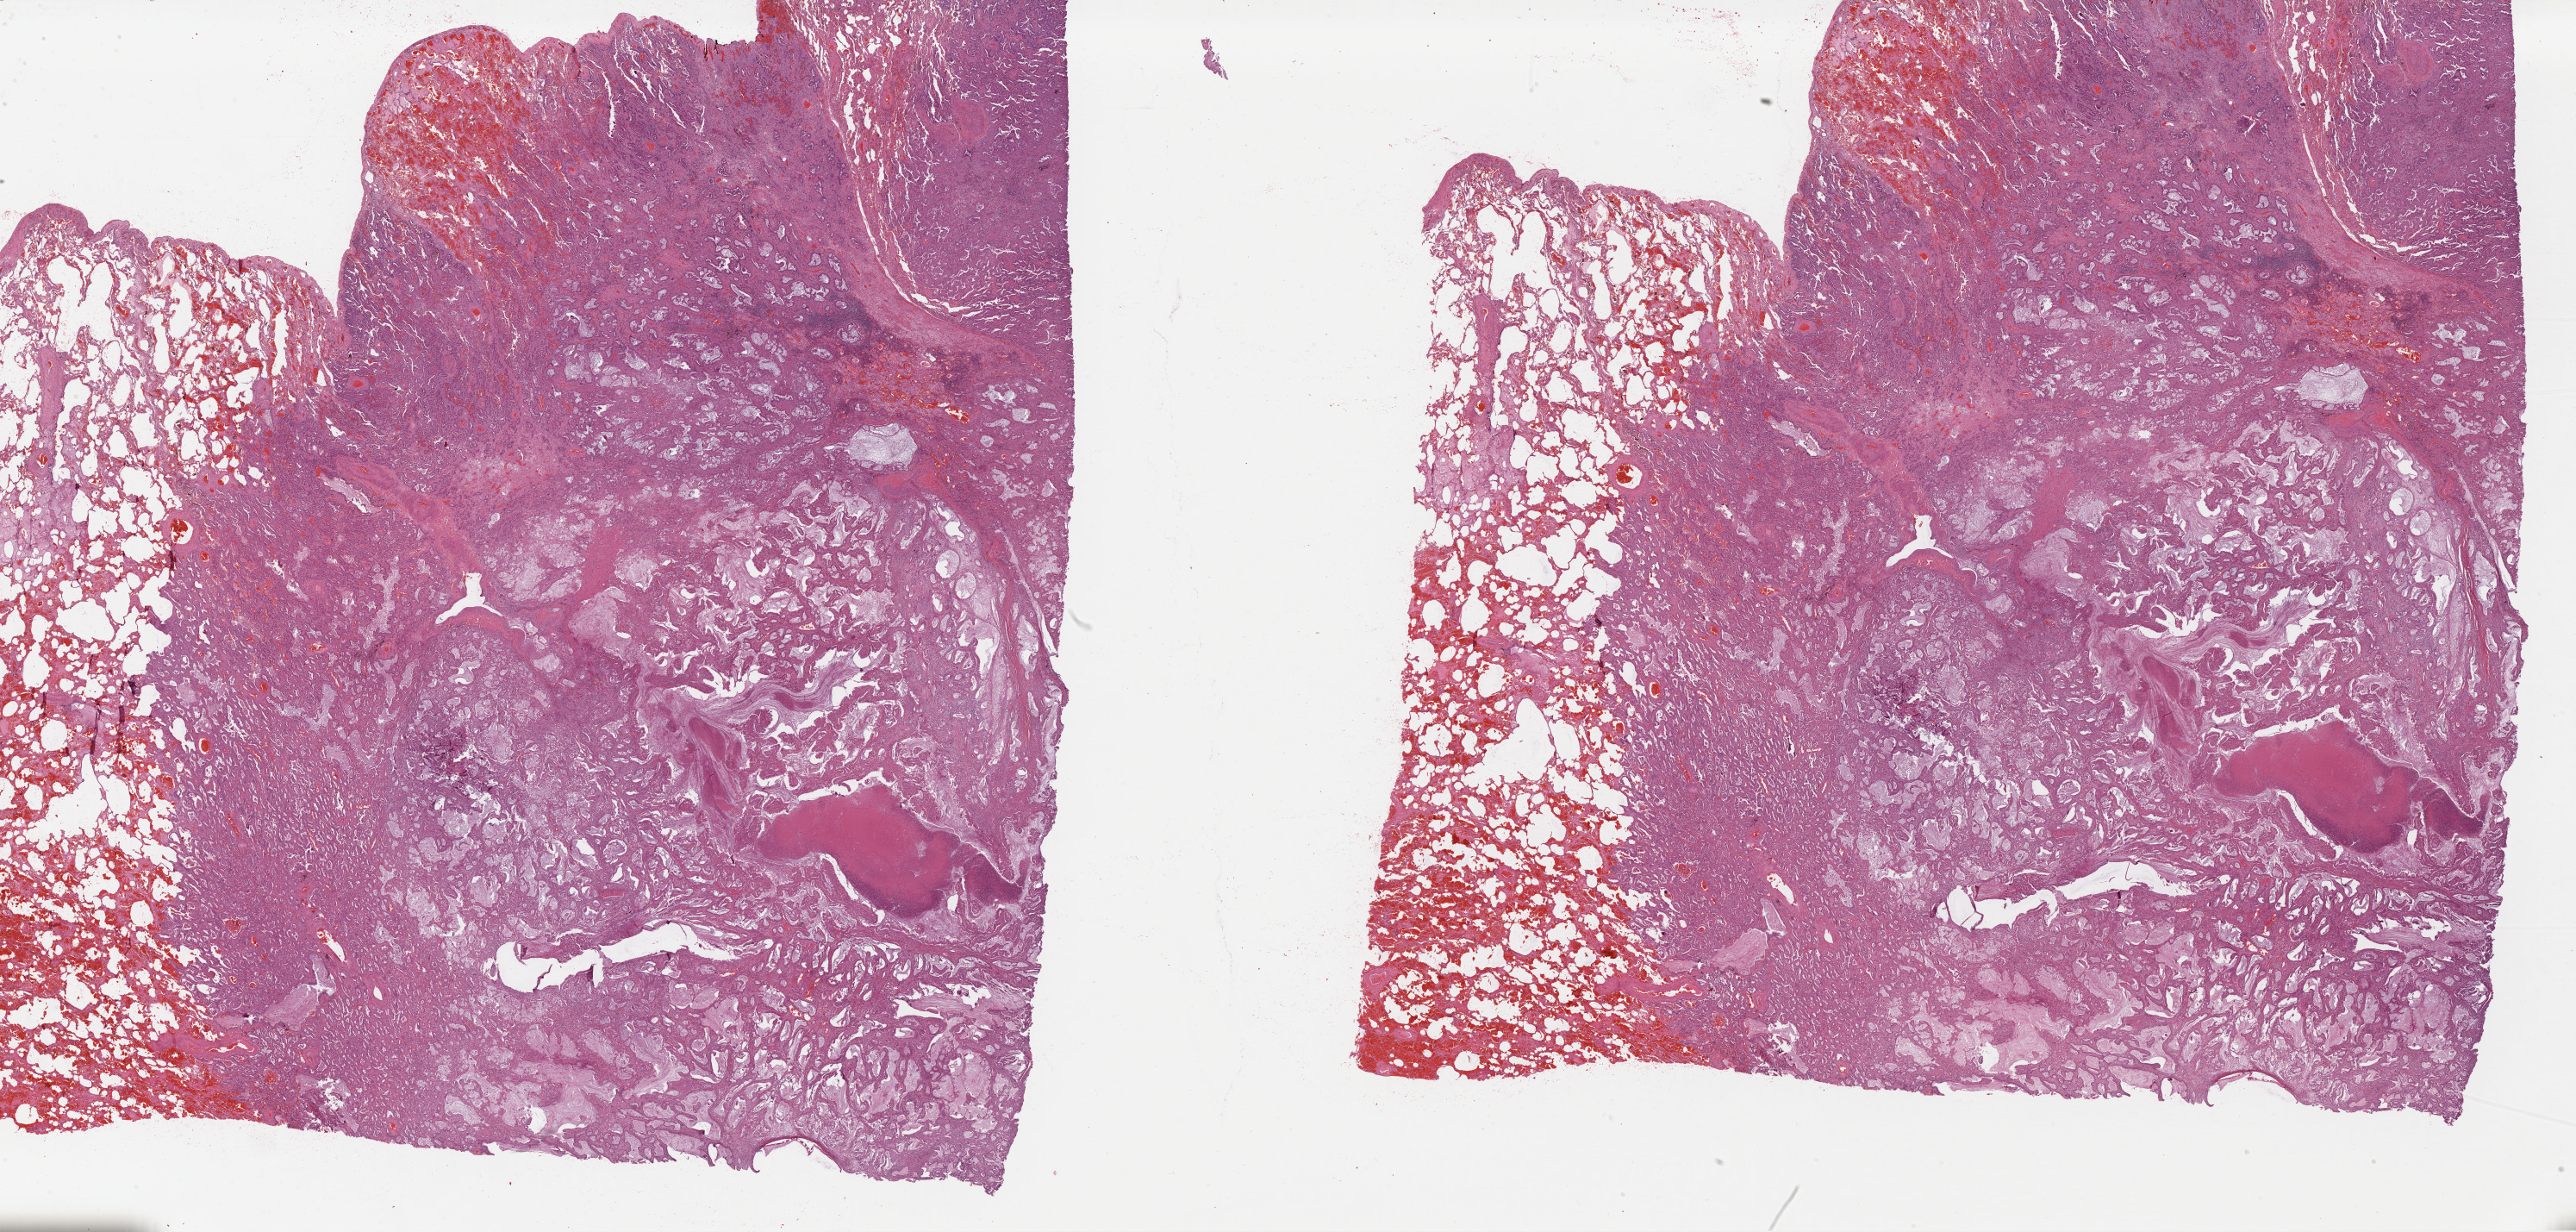
Whole-slide histology image, H&E-stained — shown as a low-resolution overview of the whole scanned area (about 47.0 x 22.5 mm). FFPE section. Primary tumour sample from the lung. Female, age 65 years at initial diagnosis.
Diagnosis: Adenocarcinoma, NOS (upper lobe, lung).